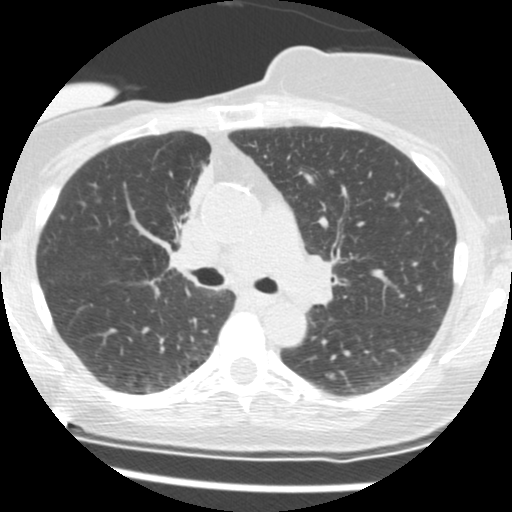
Chest CT (low-dose screening protocol), one axial image, second screening round (one year after baseline), lung window (W 1500 / L -600 HU), 120 kVp, slice 53 of 165 in the series. Female, age 56 years at enrolment.
Expert reader's lesion annotation, box from (x=152, y=165) to (x=207, y=258) px. The screening reader recorded 2 non-calcified nodules or masses ≥4 mm on this exam; which of them this box marks is not recorded. Lung cancer was diagnosed 675 days after this screen (after the third annual screen): adenocarcinoma, NOS, right upper lobe, stage IIIB (AJCC 6th edition), 8 mm at pathology.